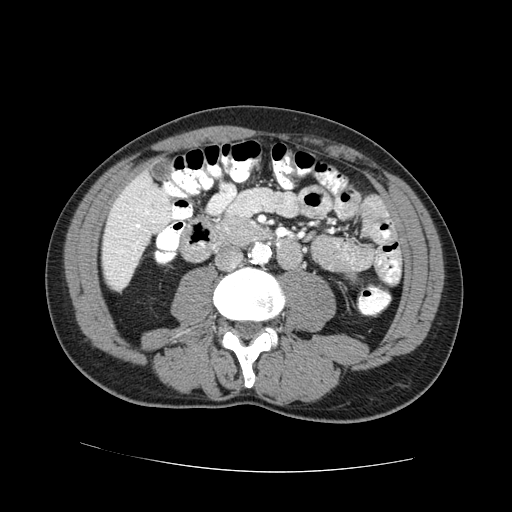
Contrast-enhanced abdominal CT (liver protocol), one axial slice. Position 12 of 73 along the scan axis. 100 kVp. One of 2 acquisitions stored at this slice position. Soft-tissue window (W 400 / L 40 HU). 2.5 mm slice thickness. 512 × 512 image matrix, field of view 380 × 380 mm. Case-level facts recorded for this patient, not image findings: diagnosis: hepatocellular carcinoma (patient treated with transarterial chemoembolisation; whether this scan precedes or follows treatment is not stated here); TNM stage (as recorded): Stage-IVA; Child-Pugh class: A.
Structures marked on this image (semi-automatically segmented with operator editing):
- liver parenchyma outside the tumour (the mass and vessels are separate outlines, so this box may not span the whole liver): bounding box [x1, y1, x2, y2] px = [102, 170, 170, 290]
- liver vessels: [136, 209, 149, 228]